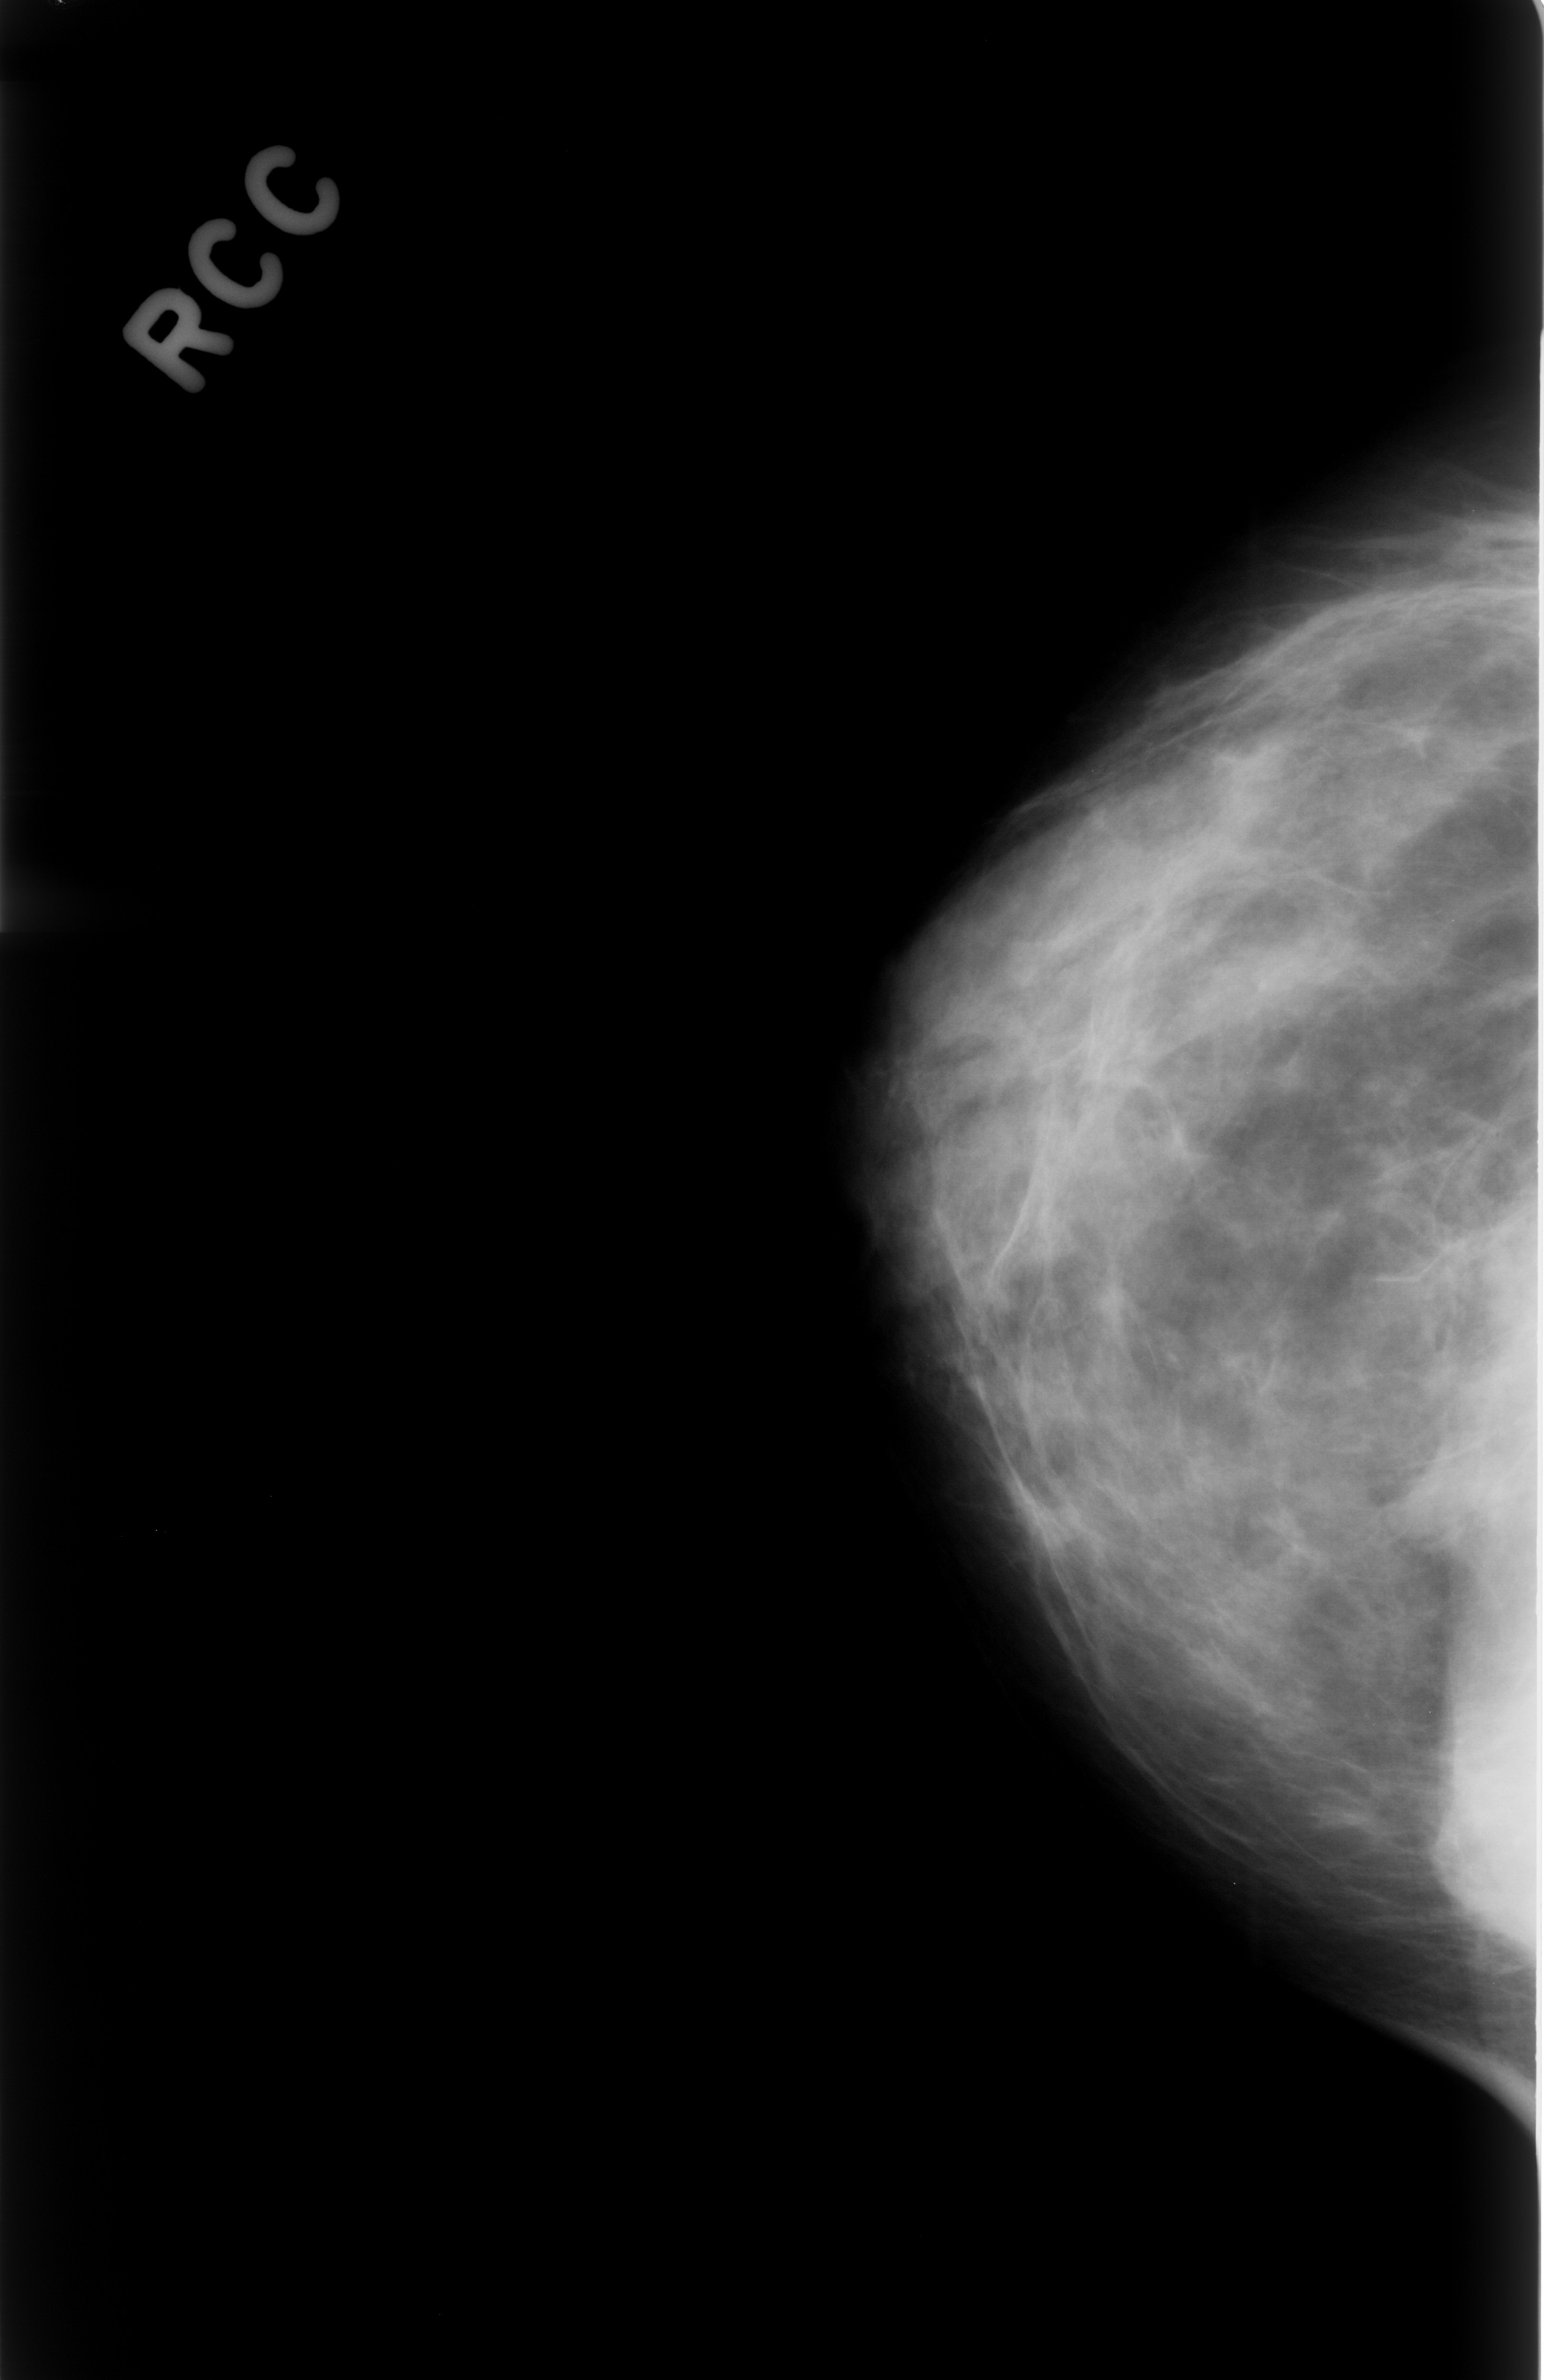
Scanned film-screen mammogram; right breast; craniocaudal (CC) view; BI-RADS breast density category 3 (scale 1–4).
Radiologist-marked abnormalities on this image: mass, shape oval, margins ill defined; BI-RADS assessment category 4; subtlety rating 3 on a 1 (subtle) to 5 (obvious) scale; pathology (as recorded): benign.